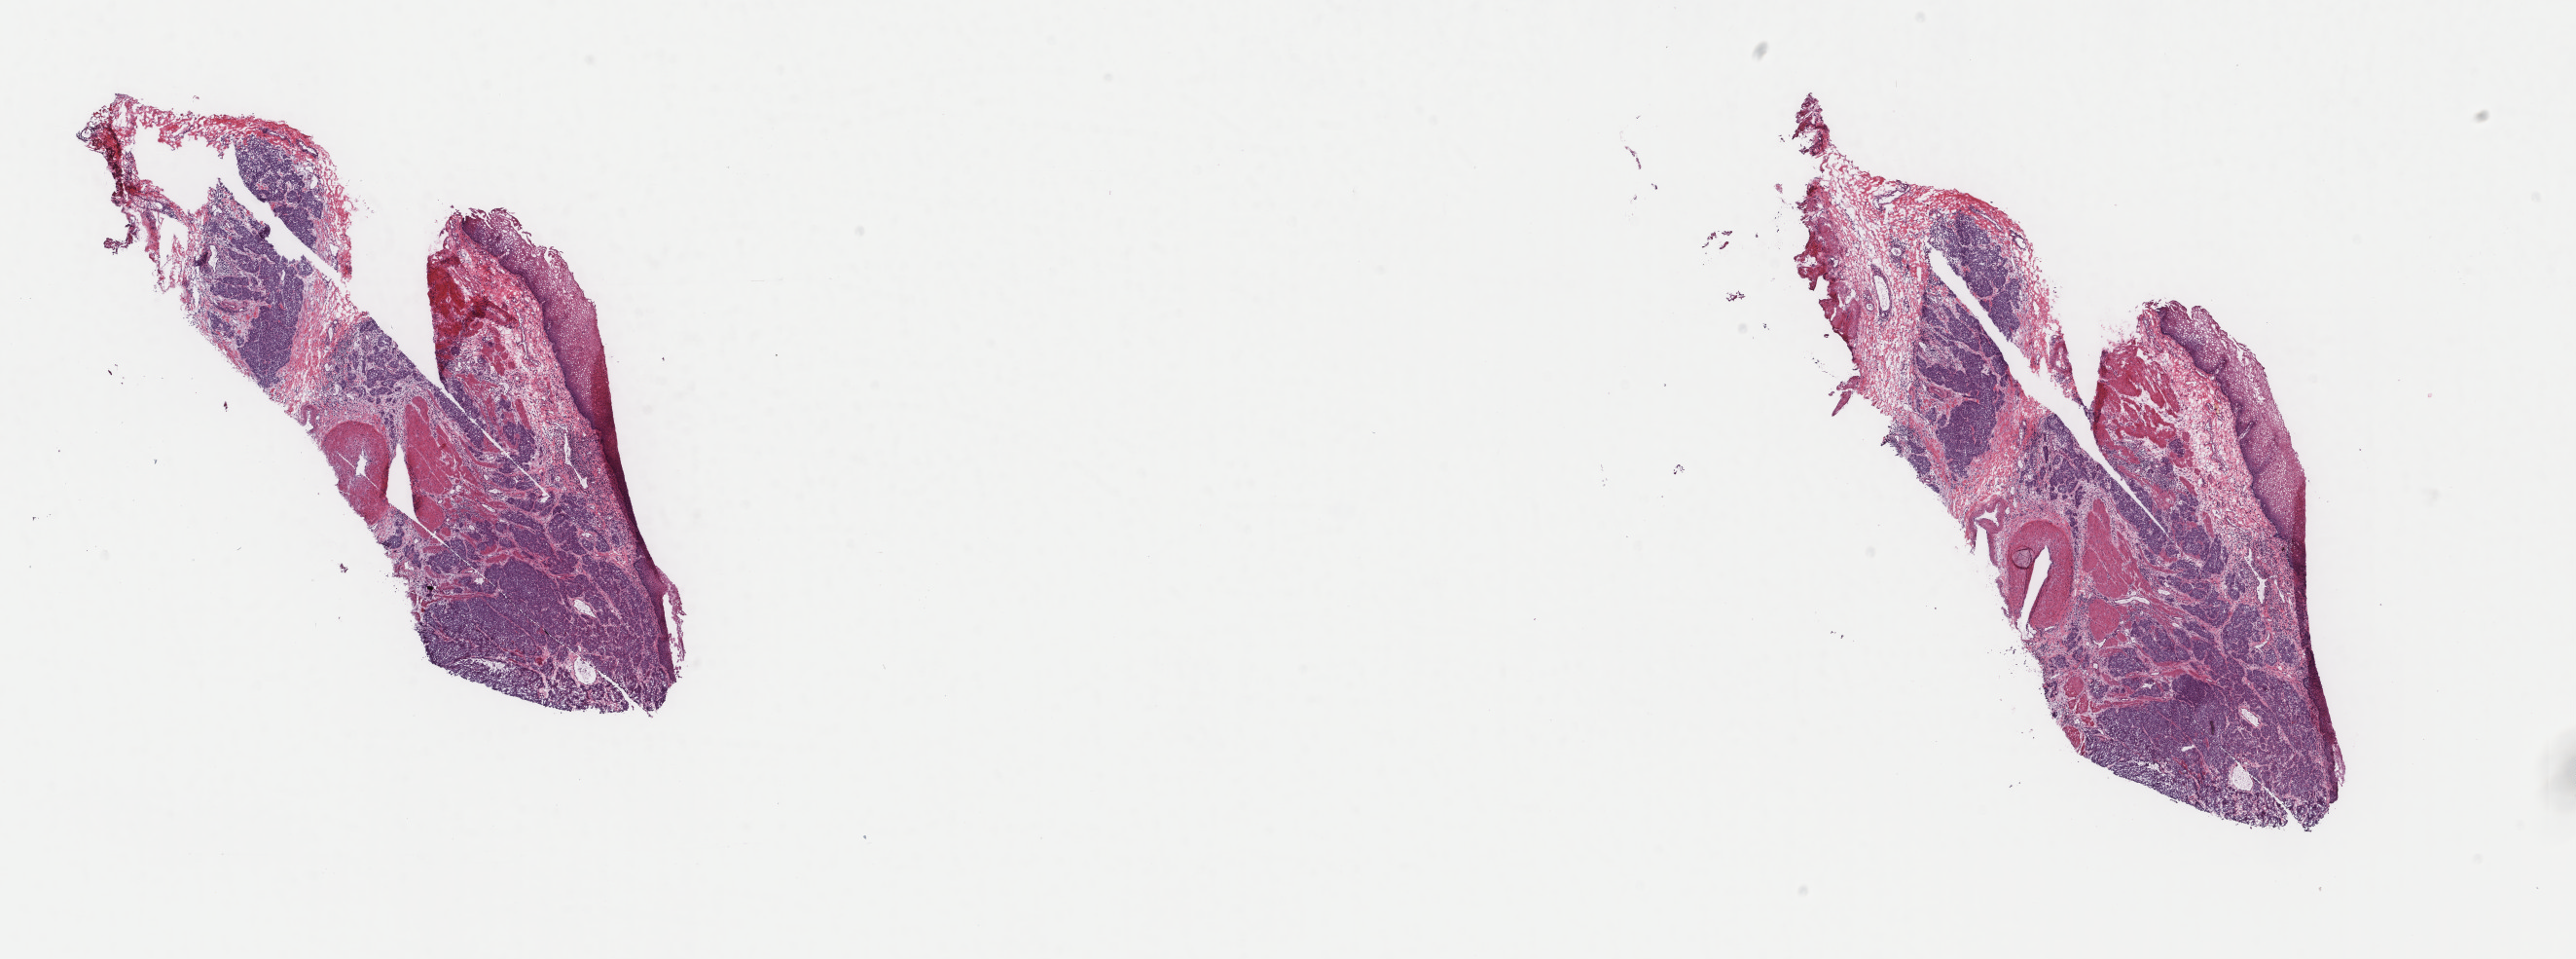
H&E whole-slide image — a low-resolution overview of the entire scanned area, about 21.0 x 7.8 mm. Frozen section from the top of the tissue portion. Esophagus, primary tumour sample. Patient: male, age at initial diagnosis 60 years. Histologic grade: G2 (moderately differentiated). Pathologist review of this section (percent, as recorded): tumour cells 75%, tumour nuclei 75%, normal cells 6%, stromal cells 19%, necrosis 0%. Infiltration values recorded for this section: lymphocyte infiltration 3%, monocyte infiltration 1%, neutrophil infiltration 2%.
- AJCC pathologic stage: IIIB
- lymph nodes positive (case pathology): 5 of 8 examined
- pathologic diagnosis: Squamous cell carcinoma, NOS (lower third of esophagus)